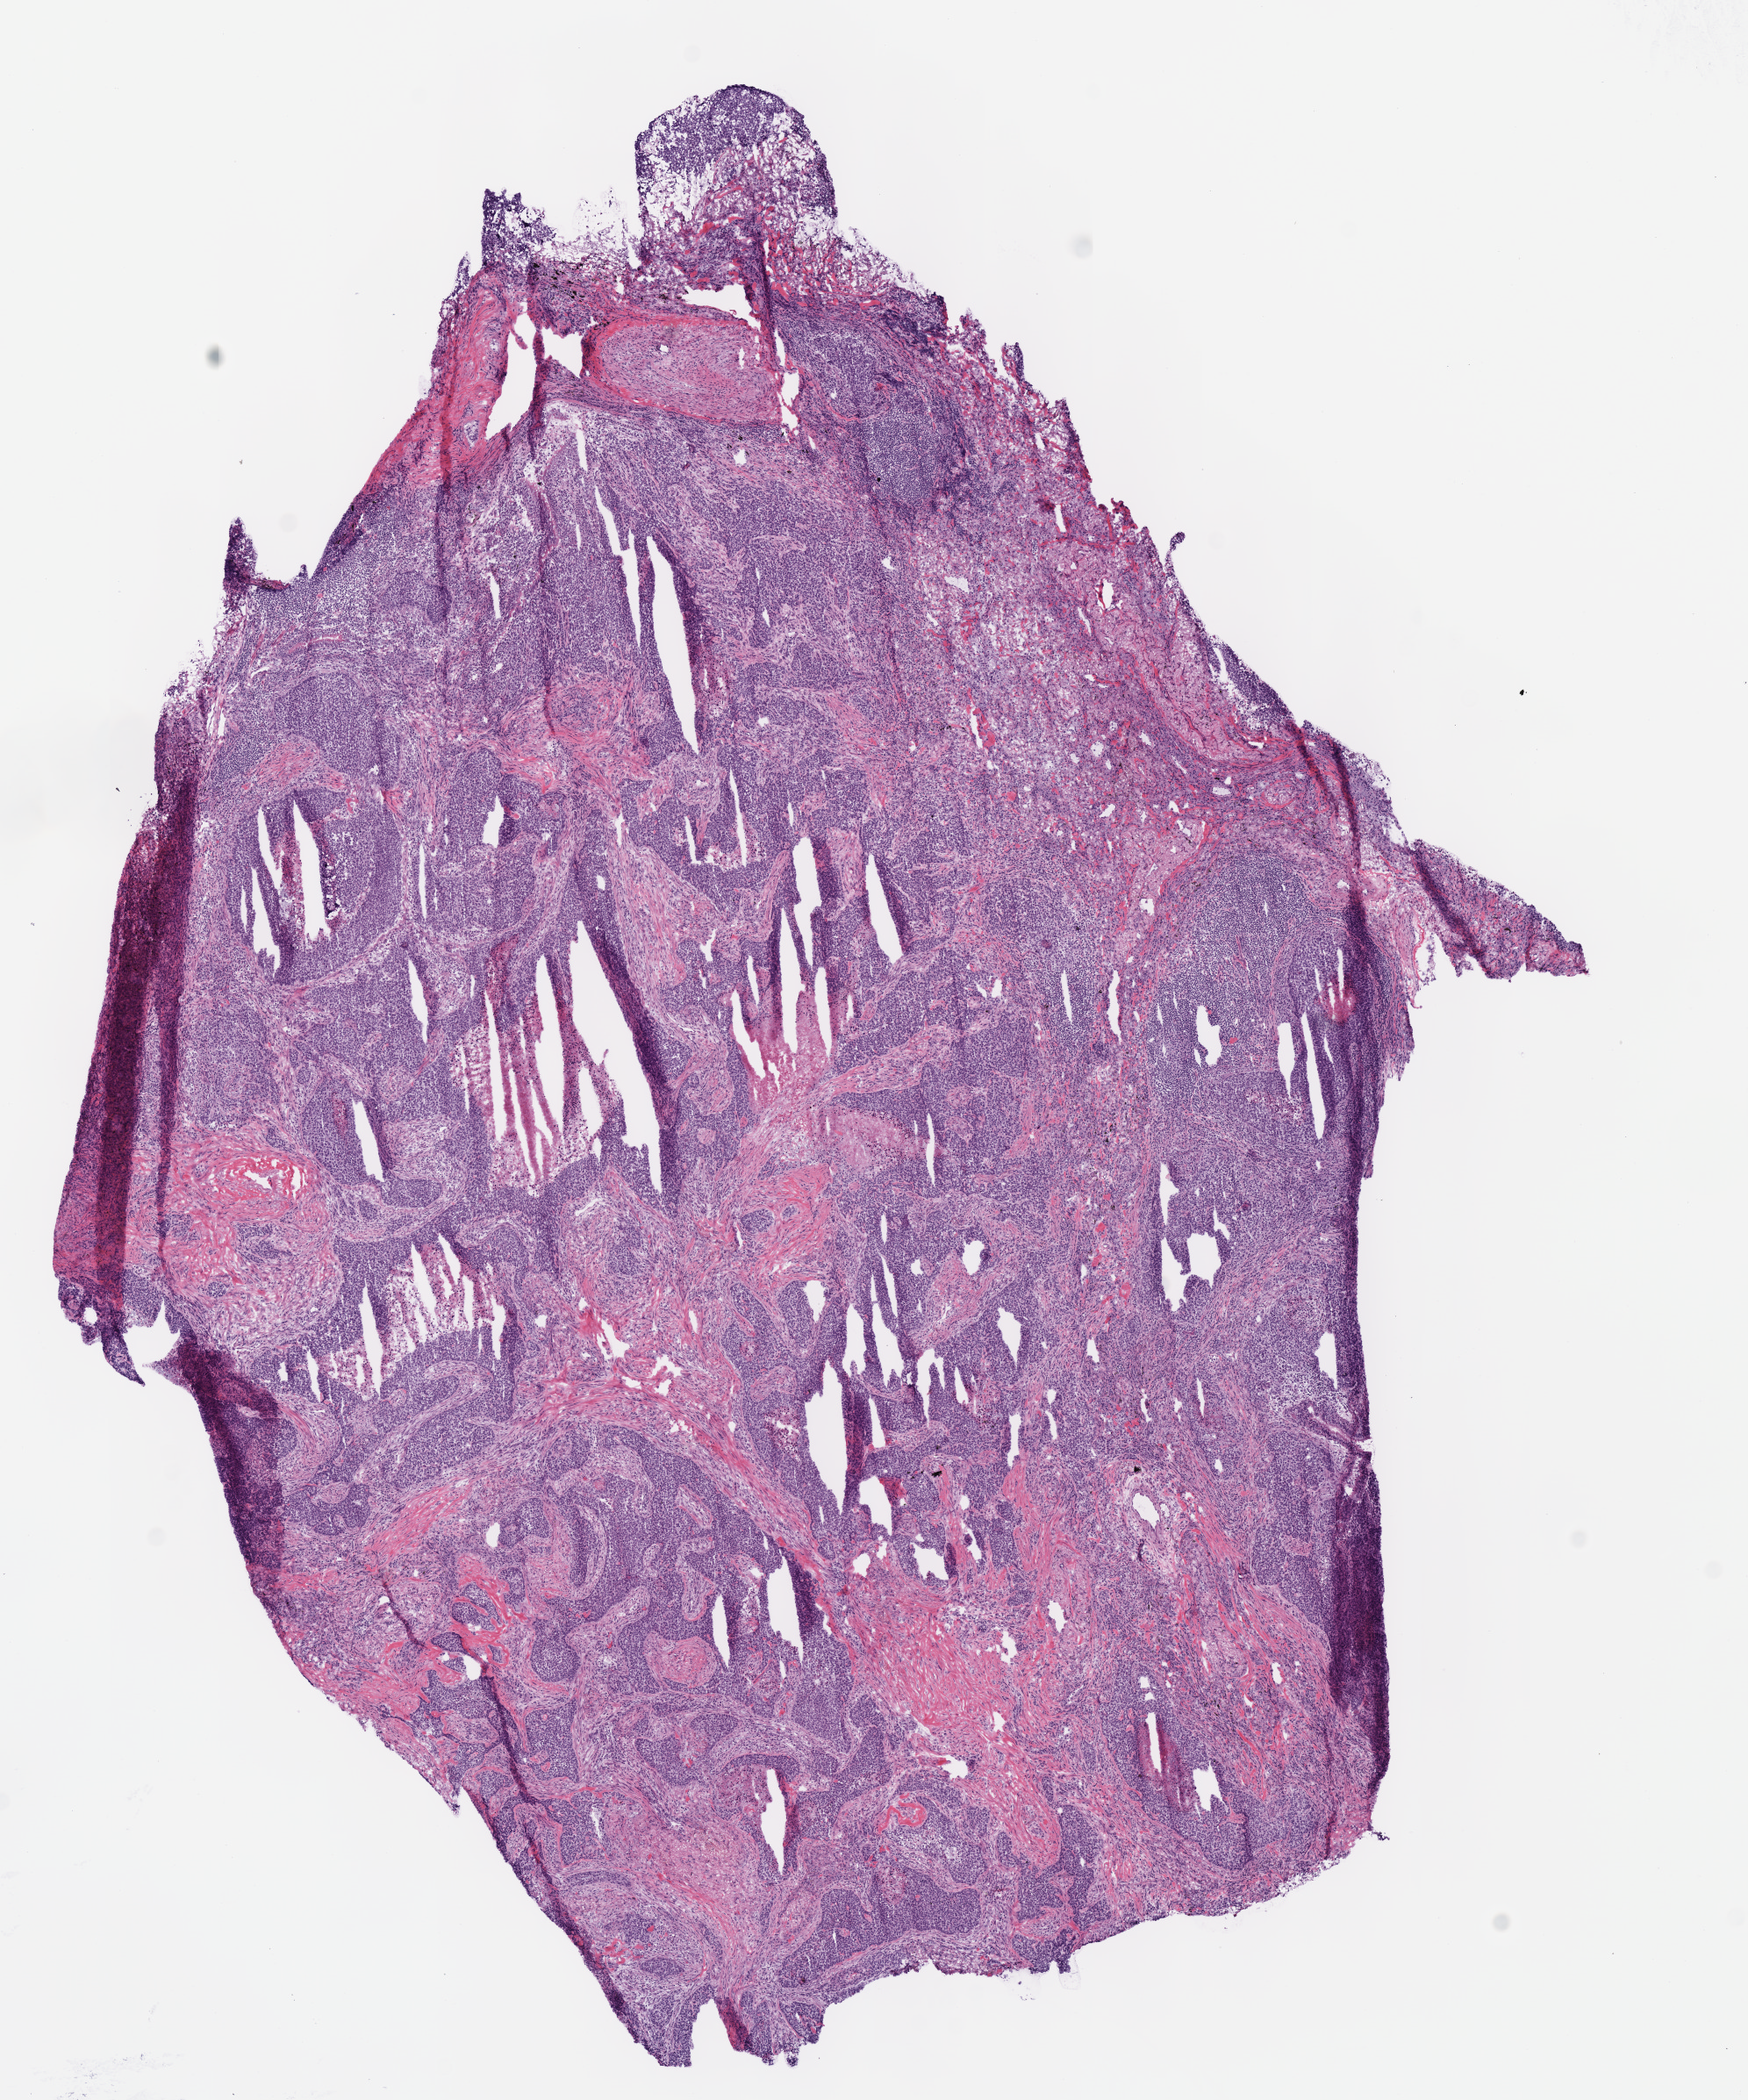
H&E-stained whole-slide image, whole scanned area (about 7.8 x 9.4 mm, from a 40x scan) shown as a low-resolution overview; frozen section from the bottom of the tissue portion; lung, primary tumour sample. Male patient; age at initial diagnosis 71 years. Slide review estimates, as recorded: tumour cells 65%, tumour nuclei 60%, normal cells 0%, stromal cells 25%, necrosis 10%.
AJCC pathologic stage: IA. Diagnosis: Squamous cell carcinoma, NOS (lower lobe, lung).